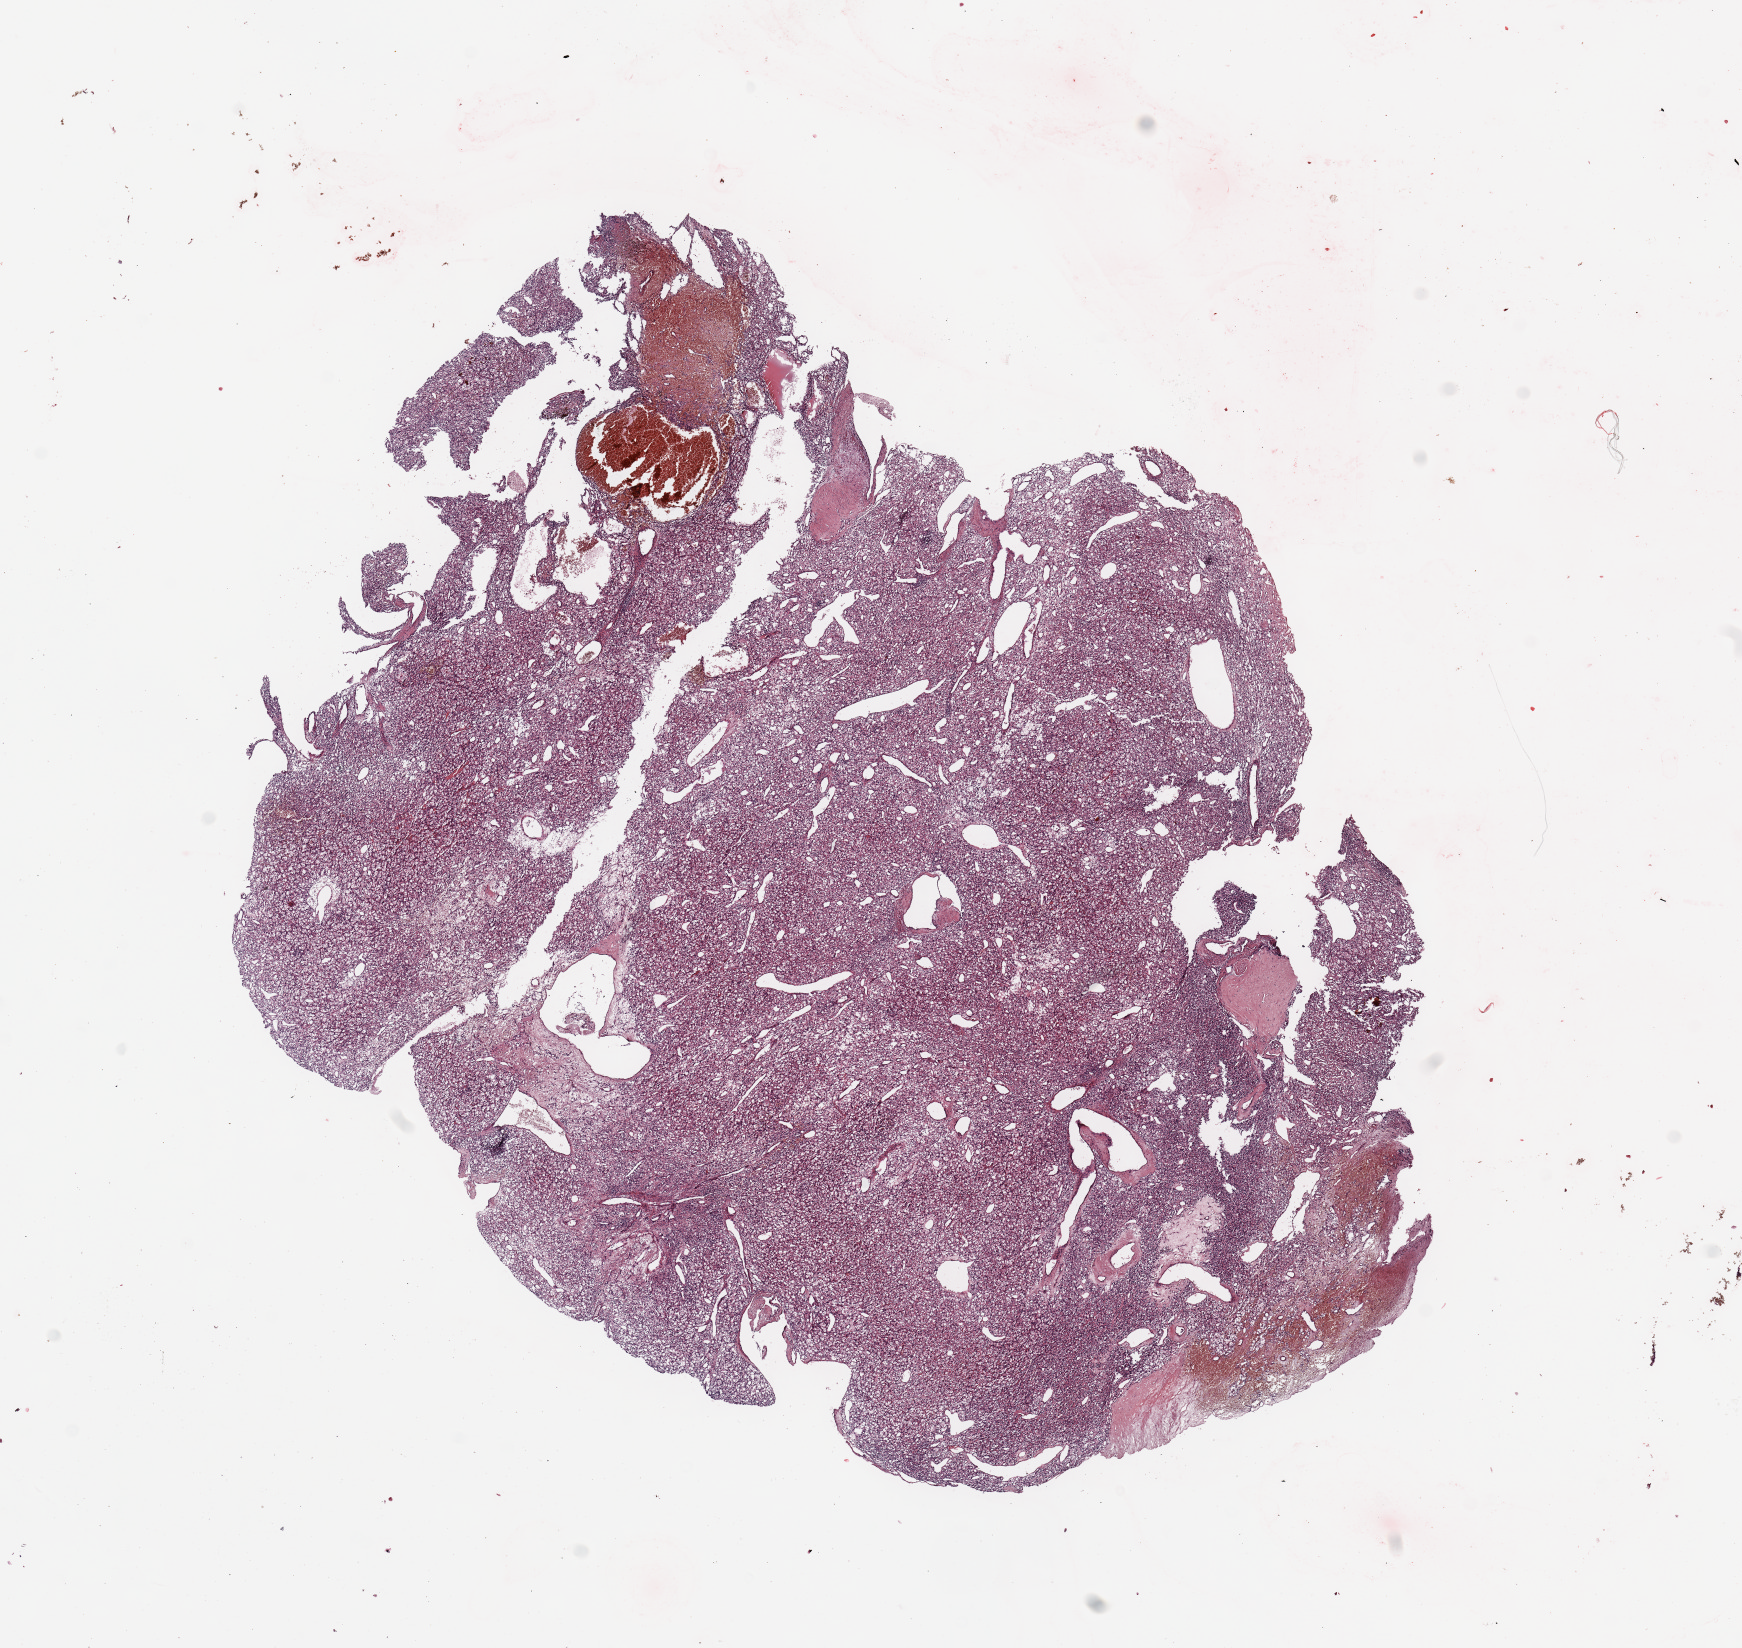
H&E whole-slide image — whole scanned area (about 13.8 x 13.0 mm, acquisition: 20x scan) shown as a low-resolution overview, tumour tissue sample, sampled site: kidney. 49-year-old male patient. Histologic grade: G2 (moderately differentiated). Pathologist review of this section (percent, as recorded): tumour nuclei 85%, necrosis 2%.
• AJCC pathologic stage: I
• primary tumour site (as recorded): upper pole
• diagnosis: Renal cell carcinoma, NOS